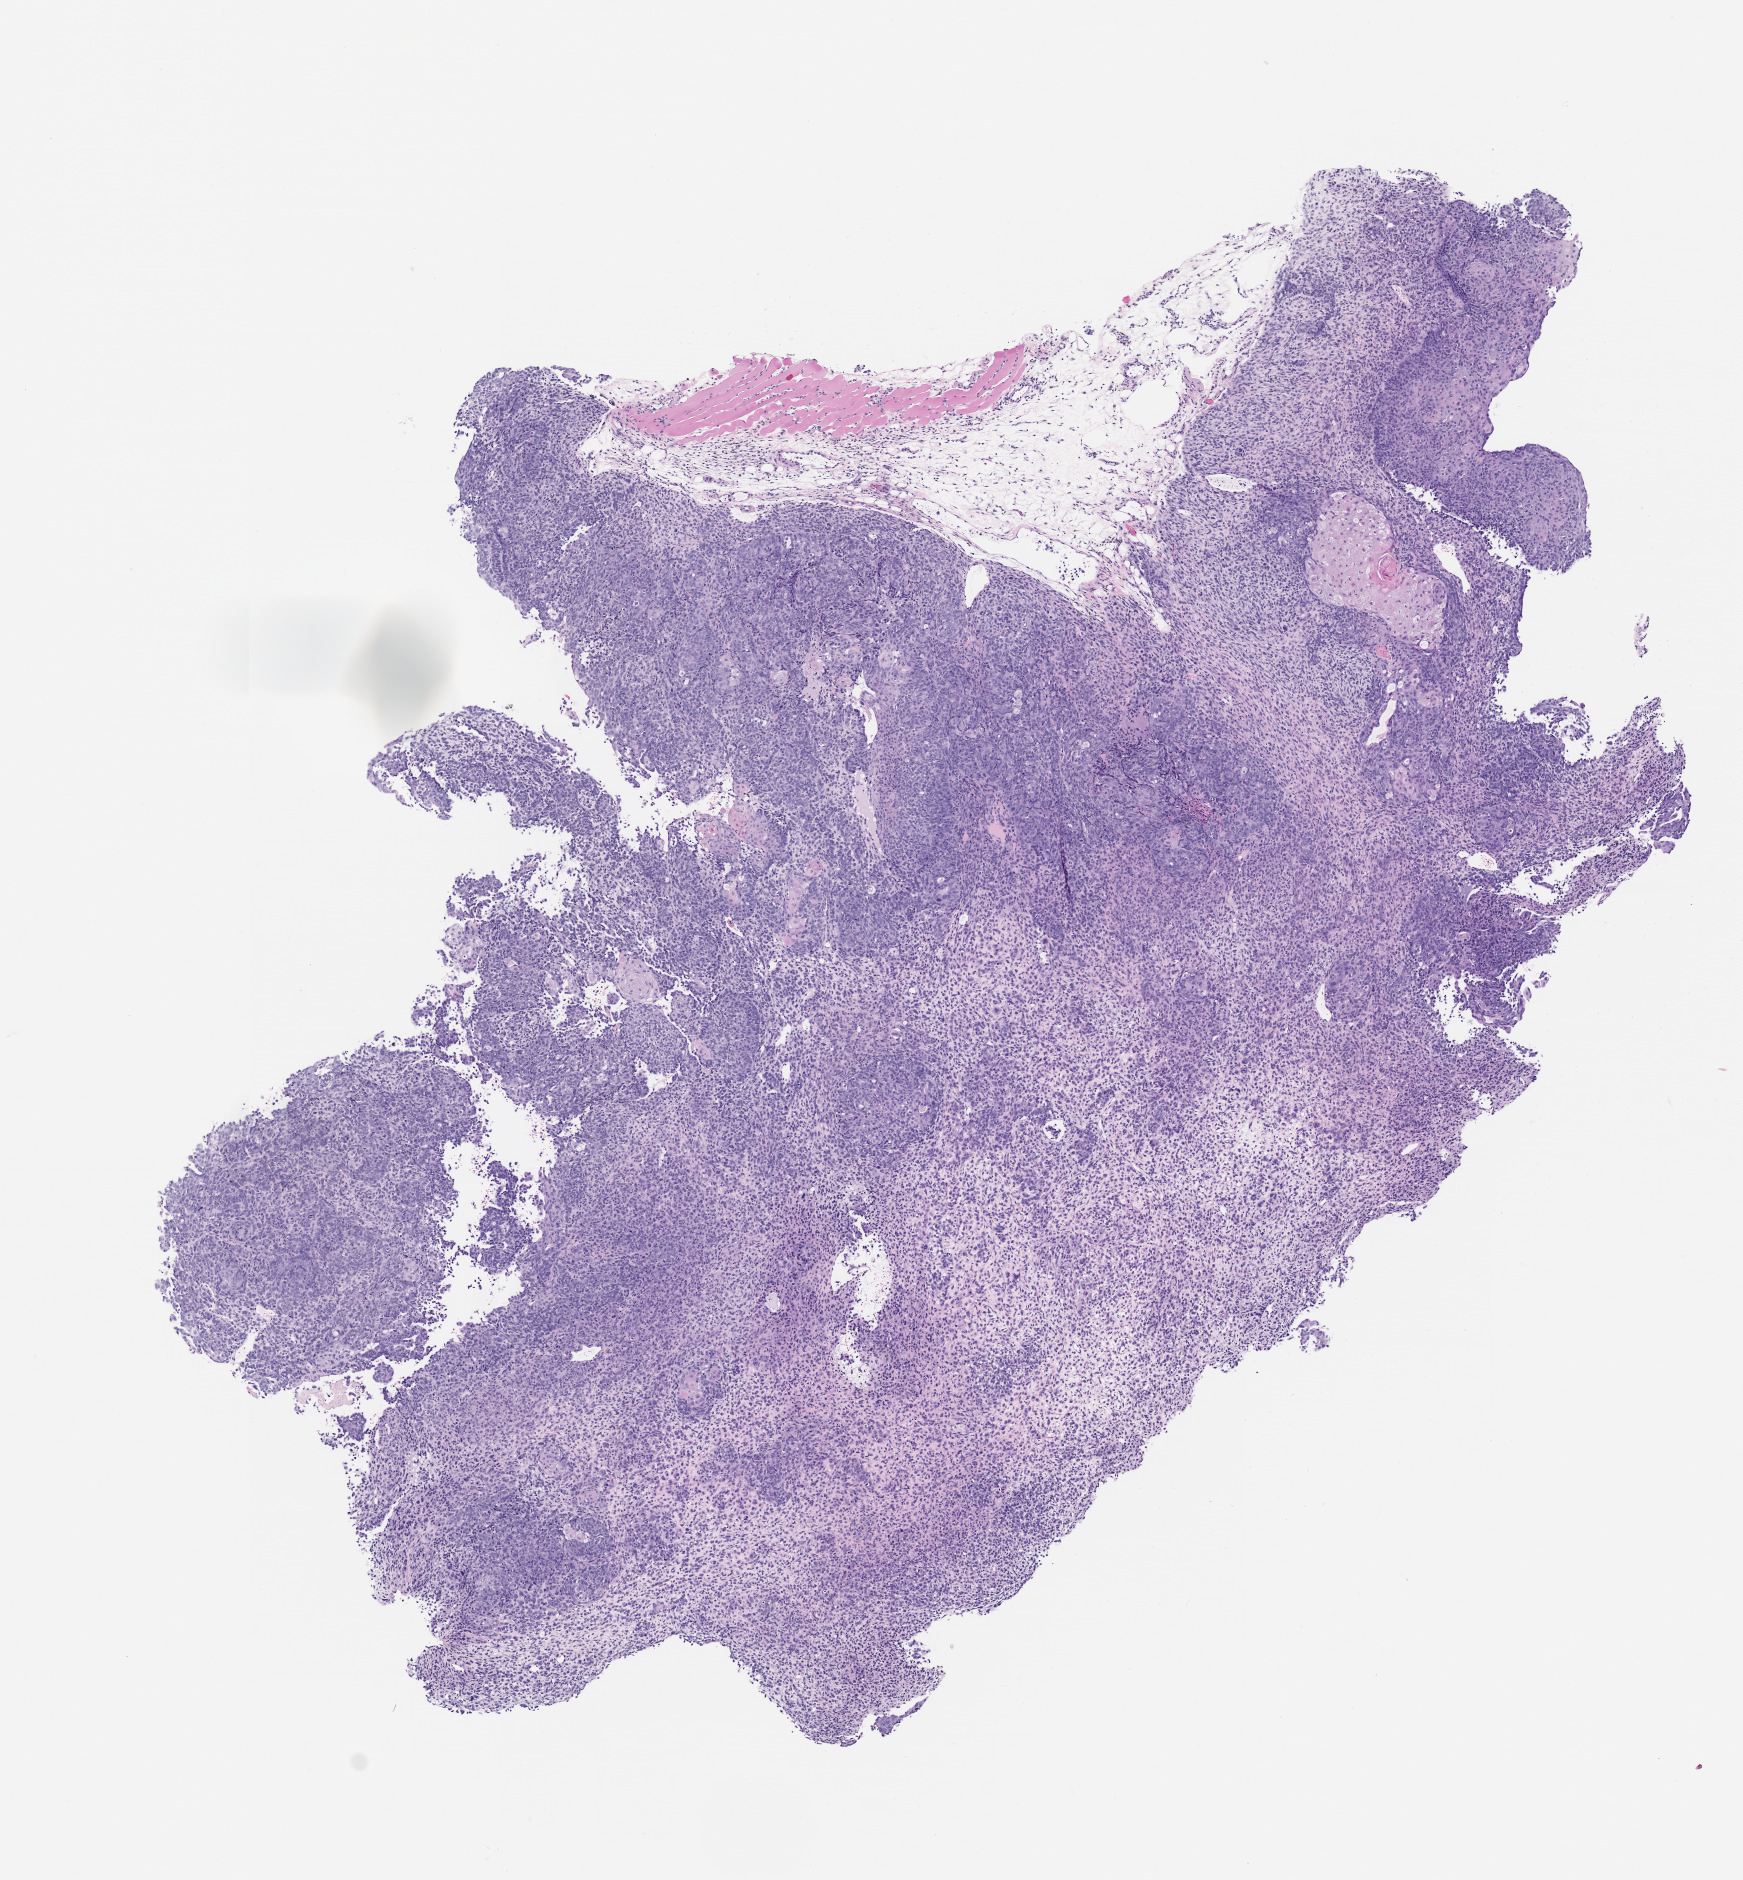
Whole-slide image, haematoxylin and eosin: patient-derived xenograft (human tumor grown in a mouse), passage 1 — shown as a low-resolution overview of the whole scanned area (about 7.0 x 7.6 mm), FFPE section, originating tumor site category: female genital tract.
- originating patient diagnosis: Carcinosarcoma